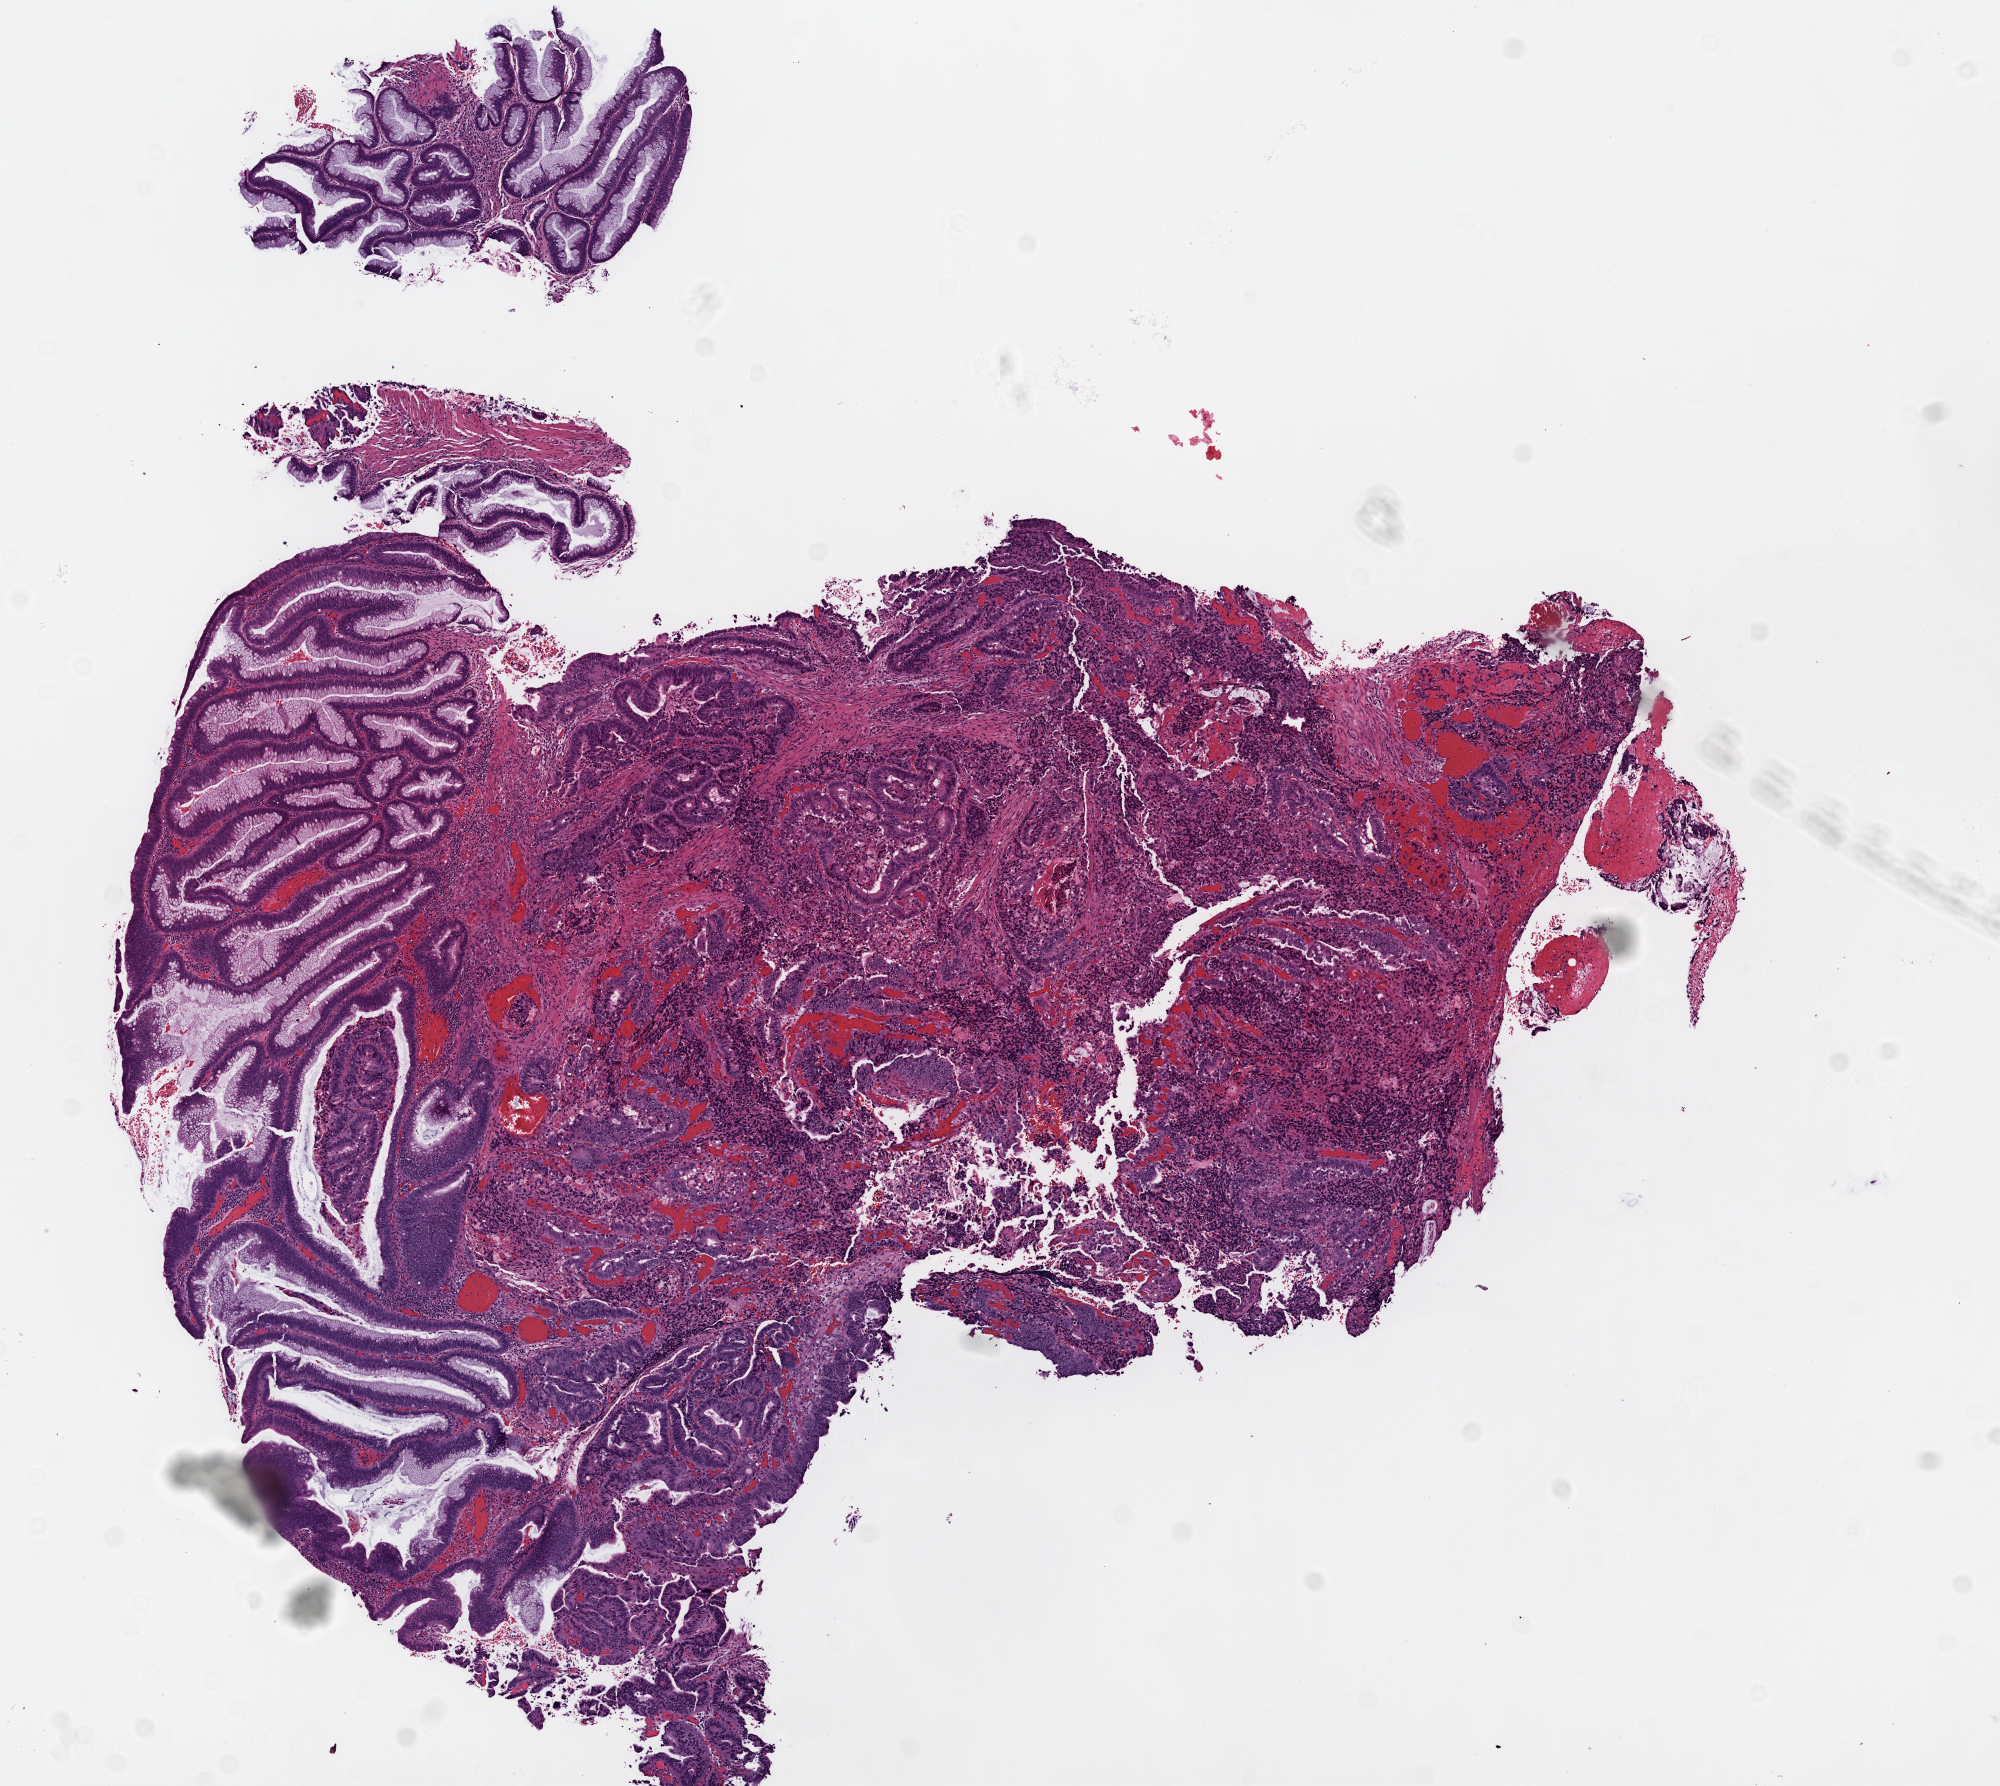
Digitized Hematoxylin and eosin (H&E) stained tissue section (whole slide), a low-resolution overview of the entire scanned area, about 8.0 x 7.2 mm. Frozen section from the top of the tissue portion. Primary tumour sample from the rectum. Female, age 48 years at initial diagnosis. Slide review estimates, as recorded: tumour cells 70%, tumour nuclei 60%, normal cells 12%, stromal cells 15%, necrosis 3%.
TNM: T1 N0 M0. Diagnosis: Adenocarcinoma, NOS (rectosigmoid junction). AJCC pathologic stage: I.